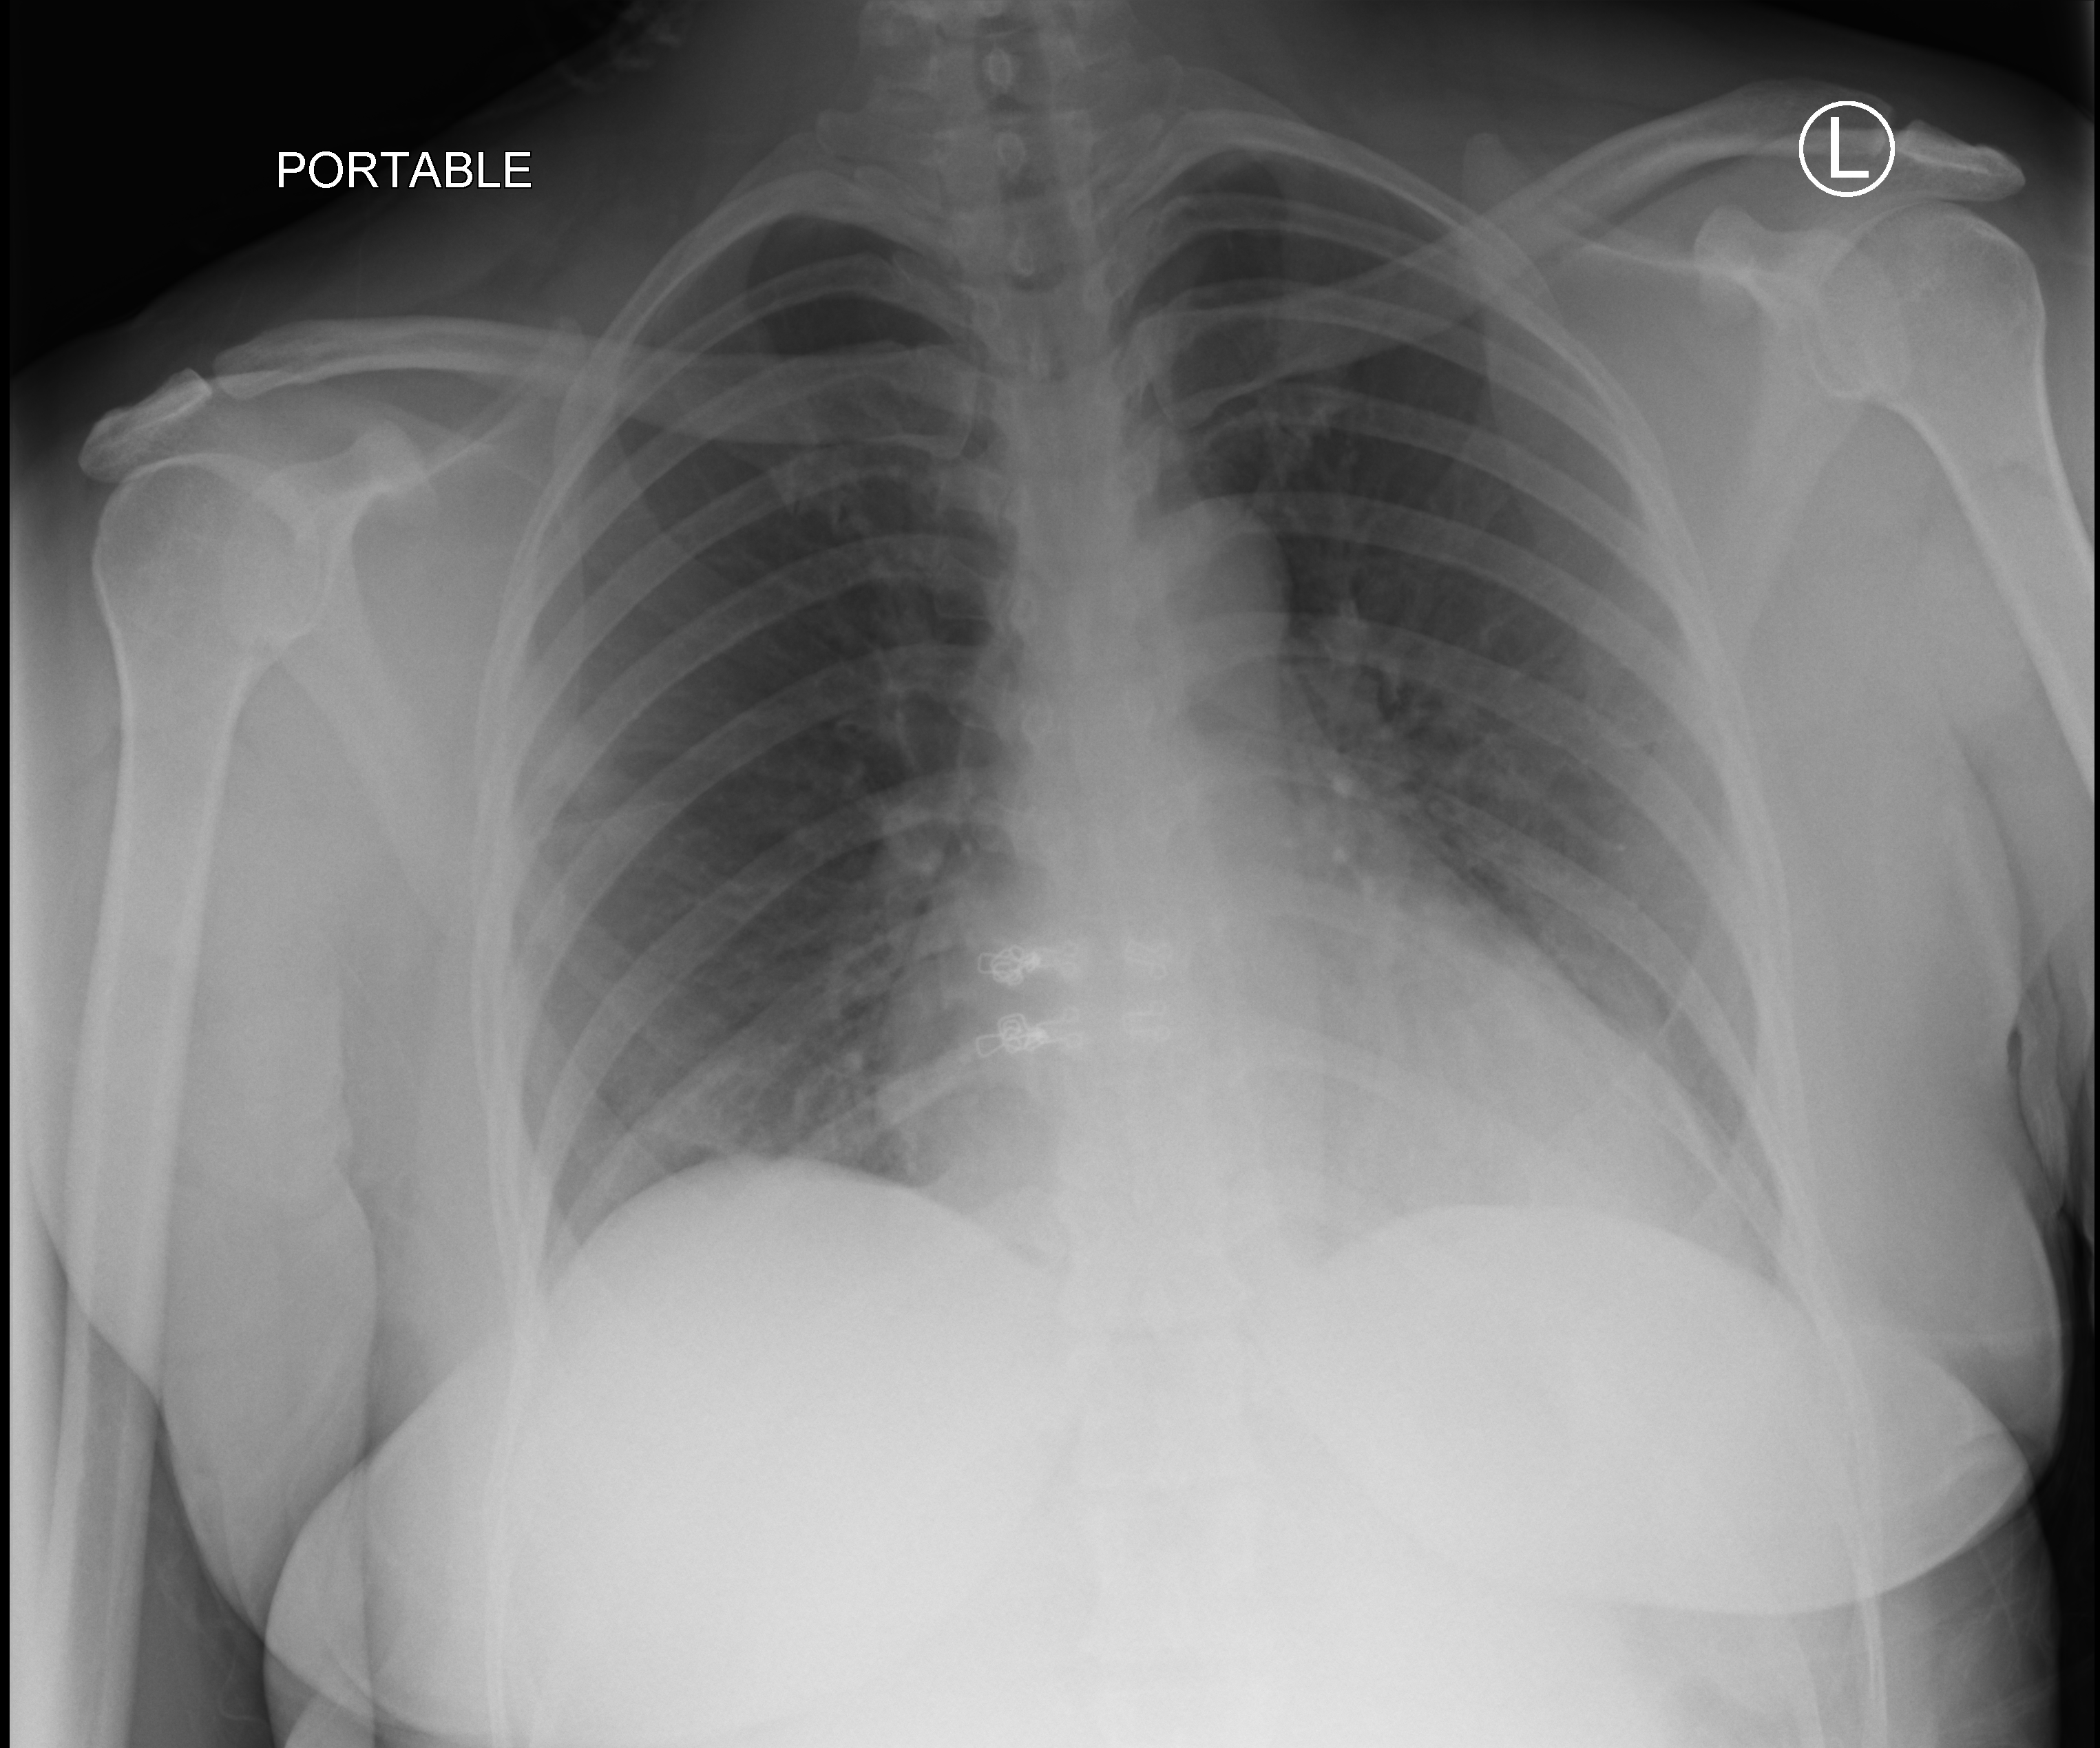
Chest X-ray (portable), anteroposterior (AP) projection. Patient hospitalised with COVID-19; female, aged 18–59 years.
From the hospital-stay record, not from the radiograph (when in the stay this image was taken is not recorded): admitted to intensive care during this hospital stay: no.